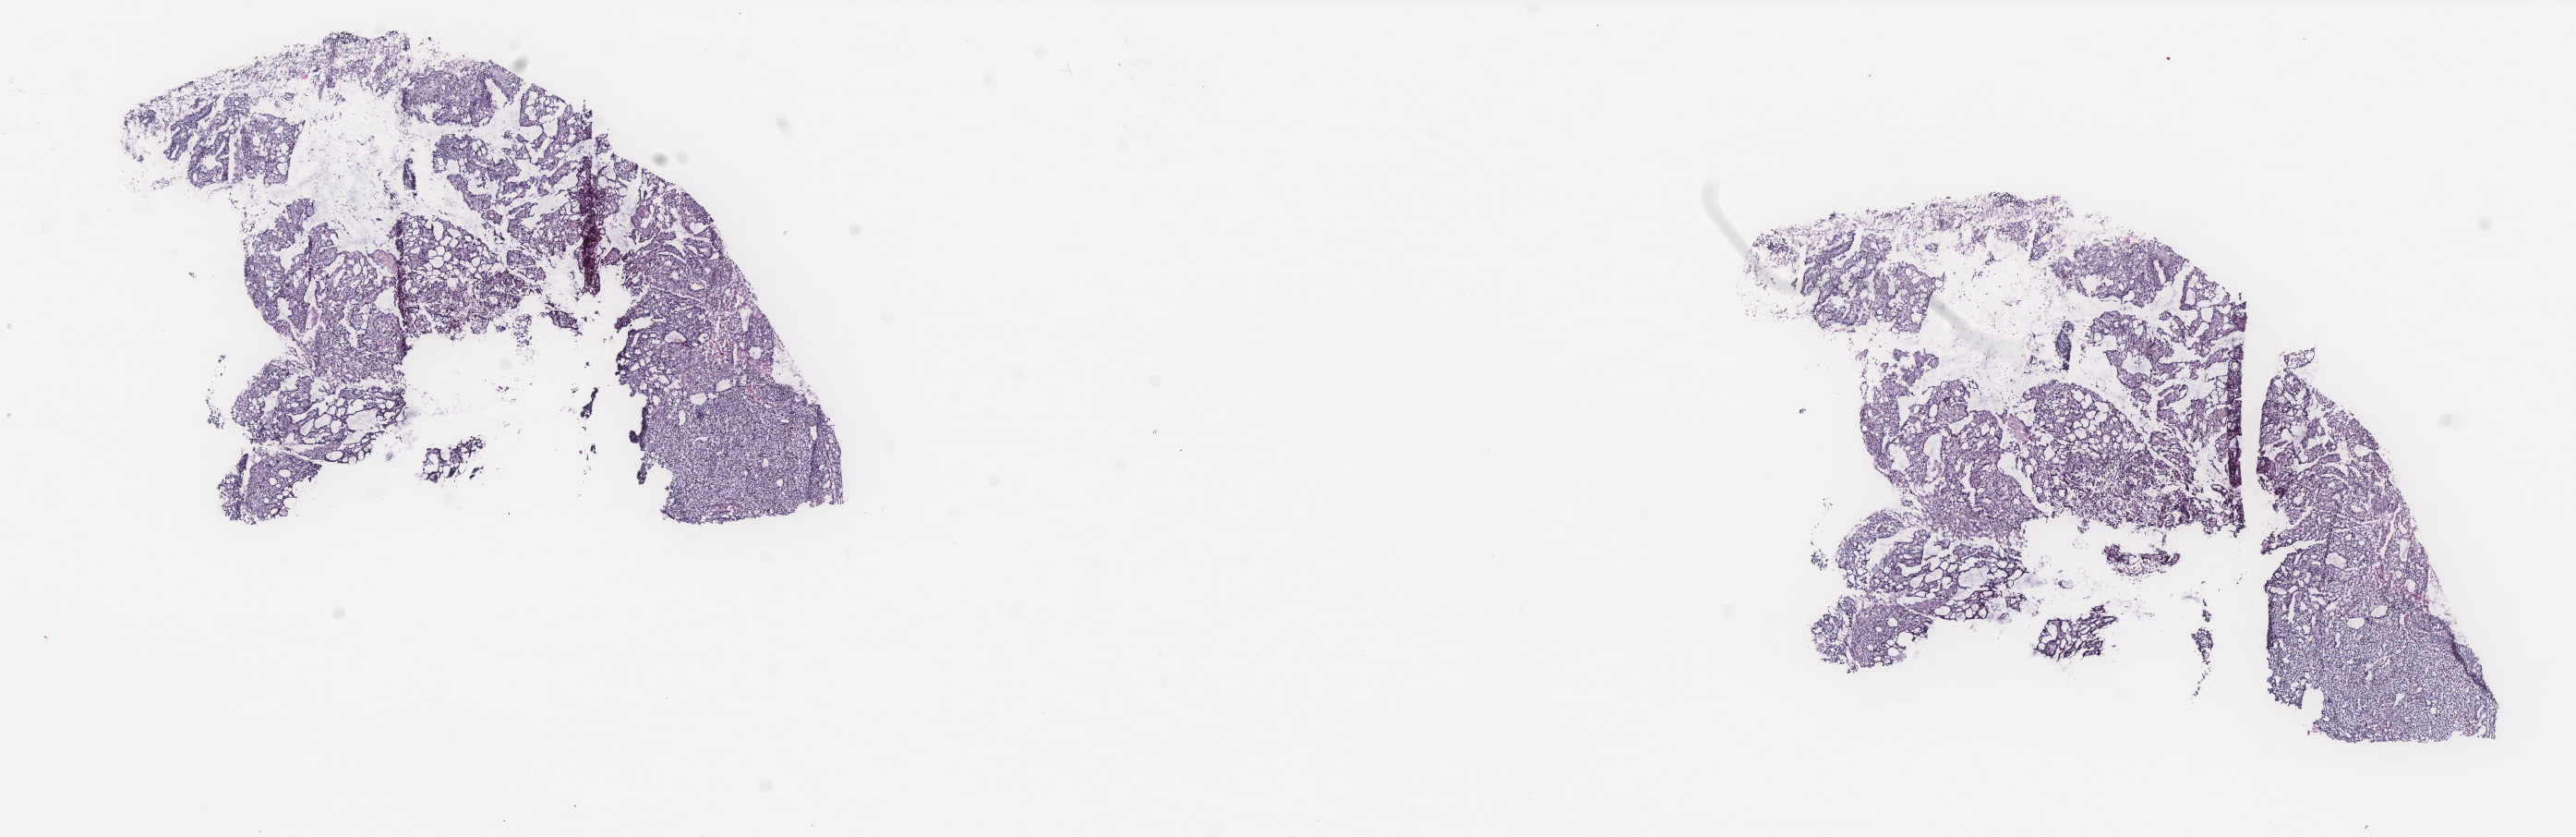
Whole-slide histology image, H&E, whole scanned area (about 22.4 x 7.3 mm, slide scanned at 40x) shown as a low-resolution overview, frozen section from the bottom of the tissue portion, uterus, primary tumour sample. Female patient; age at initial diagnosis 74 years. Histologic grade: G3 (poorly differentiated). Slide review estimates, as recorded: tumour cells 90%, tumour nuclei 100%, normal cells 0%, stromal cells 0%, necrosis 10%. Inflammatory infiltration, as recorded: lymphocyte infiltration 10%, monocyte infiltration 0%, neutrophil infiltration 10%.
- lymph nodes positive (case pathology): 0 of 14 examined
- histologic diagnosis: Endometrioid adenocarcinoma, NOS (endometrium)
- FIGO stage: IA